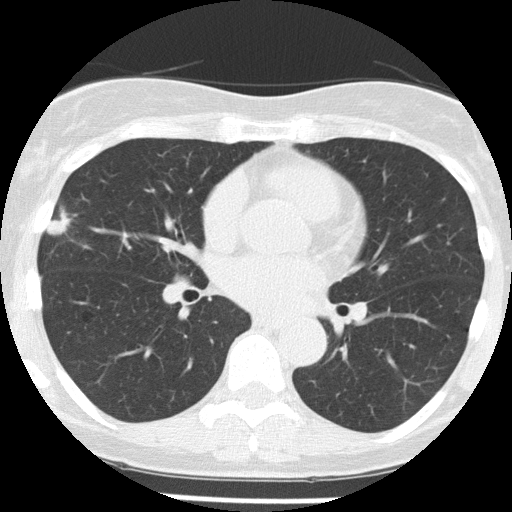
Chest CT (low-dose screening protocol), one axial image; baseline screening round; lung window (W 1500 / L -600 HU); 2 mm slice thickness; lung (sharp) reconstruction kernel (FC51); slice 75 of 156 in the series. Female participant, aged 58 years at enrolment. Former smoker at enrolment.
- Expert-annotated lung lesion, bounding box <30,195,86,254> (left, top, right, bottom; pixels).
- The exam's reader record, not a measurement of the box and not confirmed to be the same lesion: non-calcified nodule or mass ≥4 mm, right middle lobe, 18 × 9 mm, spiculated (stellate) margins, soft tissue attenuation.
- Official screen result: positive, change unspecified: nodule(s) >= 4 mm or enlarging nodule(s), mass(es), or other non-specific abnormalities suspicious for lung cancer.
- Later outcome: lung cancer diagnosed 79 days after this screen — non-small cell carcinoma, right middle lobe, poorly differentiated (G3), stage IA (AJCC 6th edition), 18 mm at pathology.